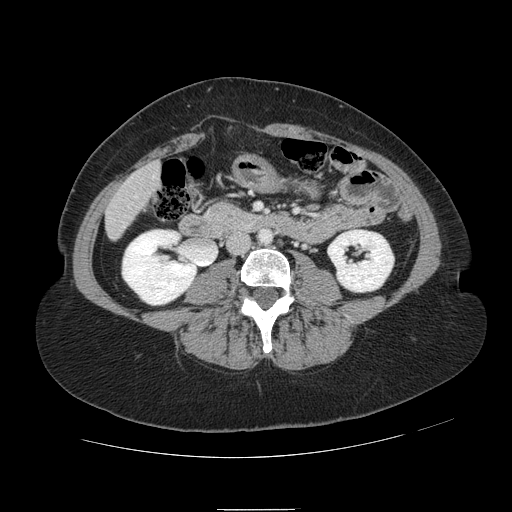
Contrast-enhanced abdominal CT, one axial slice; slice 11 of 121 in the series (ordered by position); 120 kVp; intravenous contrast given; soft-tissue window (W 400 / L 40 HU); 2.5 mm slice thickness; 512 × 512 image matrix, field of view 400 × 400 mm. Female patient, age 52 years. Case-level facts recorded for this patient, not image findings: diagnosis: colorectal cancer liver metastases, imaged before liver resection; multiple liver metastases: yes; largest metastasis: 6.3 cm; chemotherapy before resection: yes.
Structures marked on this image (outlined manually by an expert reader):
- hepatic veins: box from (x=135, y=177) to (x=155, y=197) px
- liver: (x=107, y=164)–(x=160, y=238)